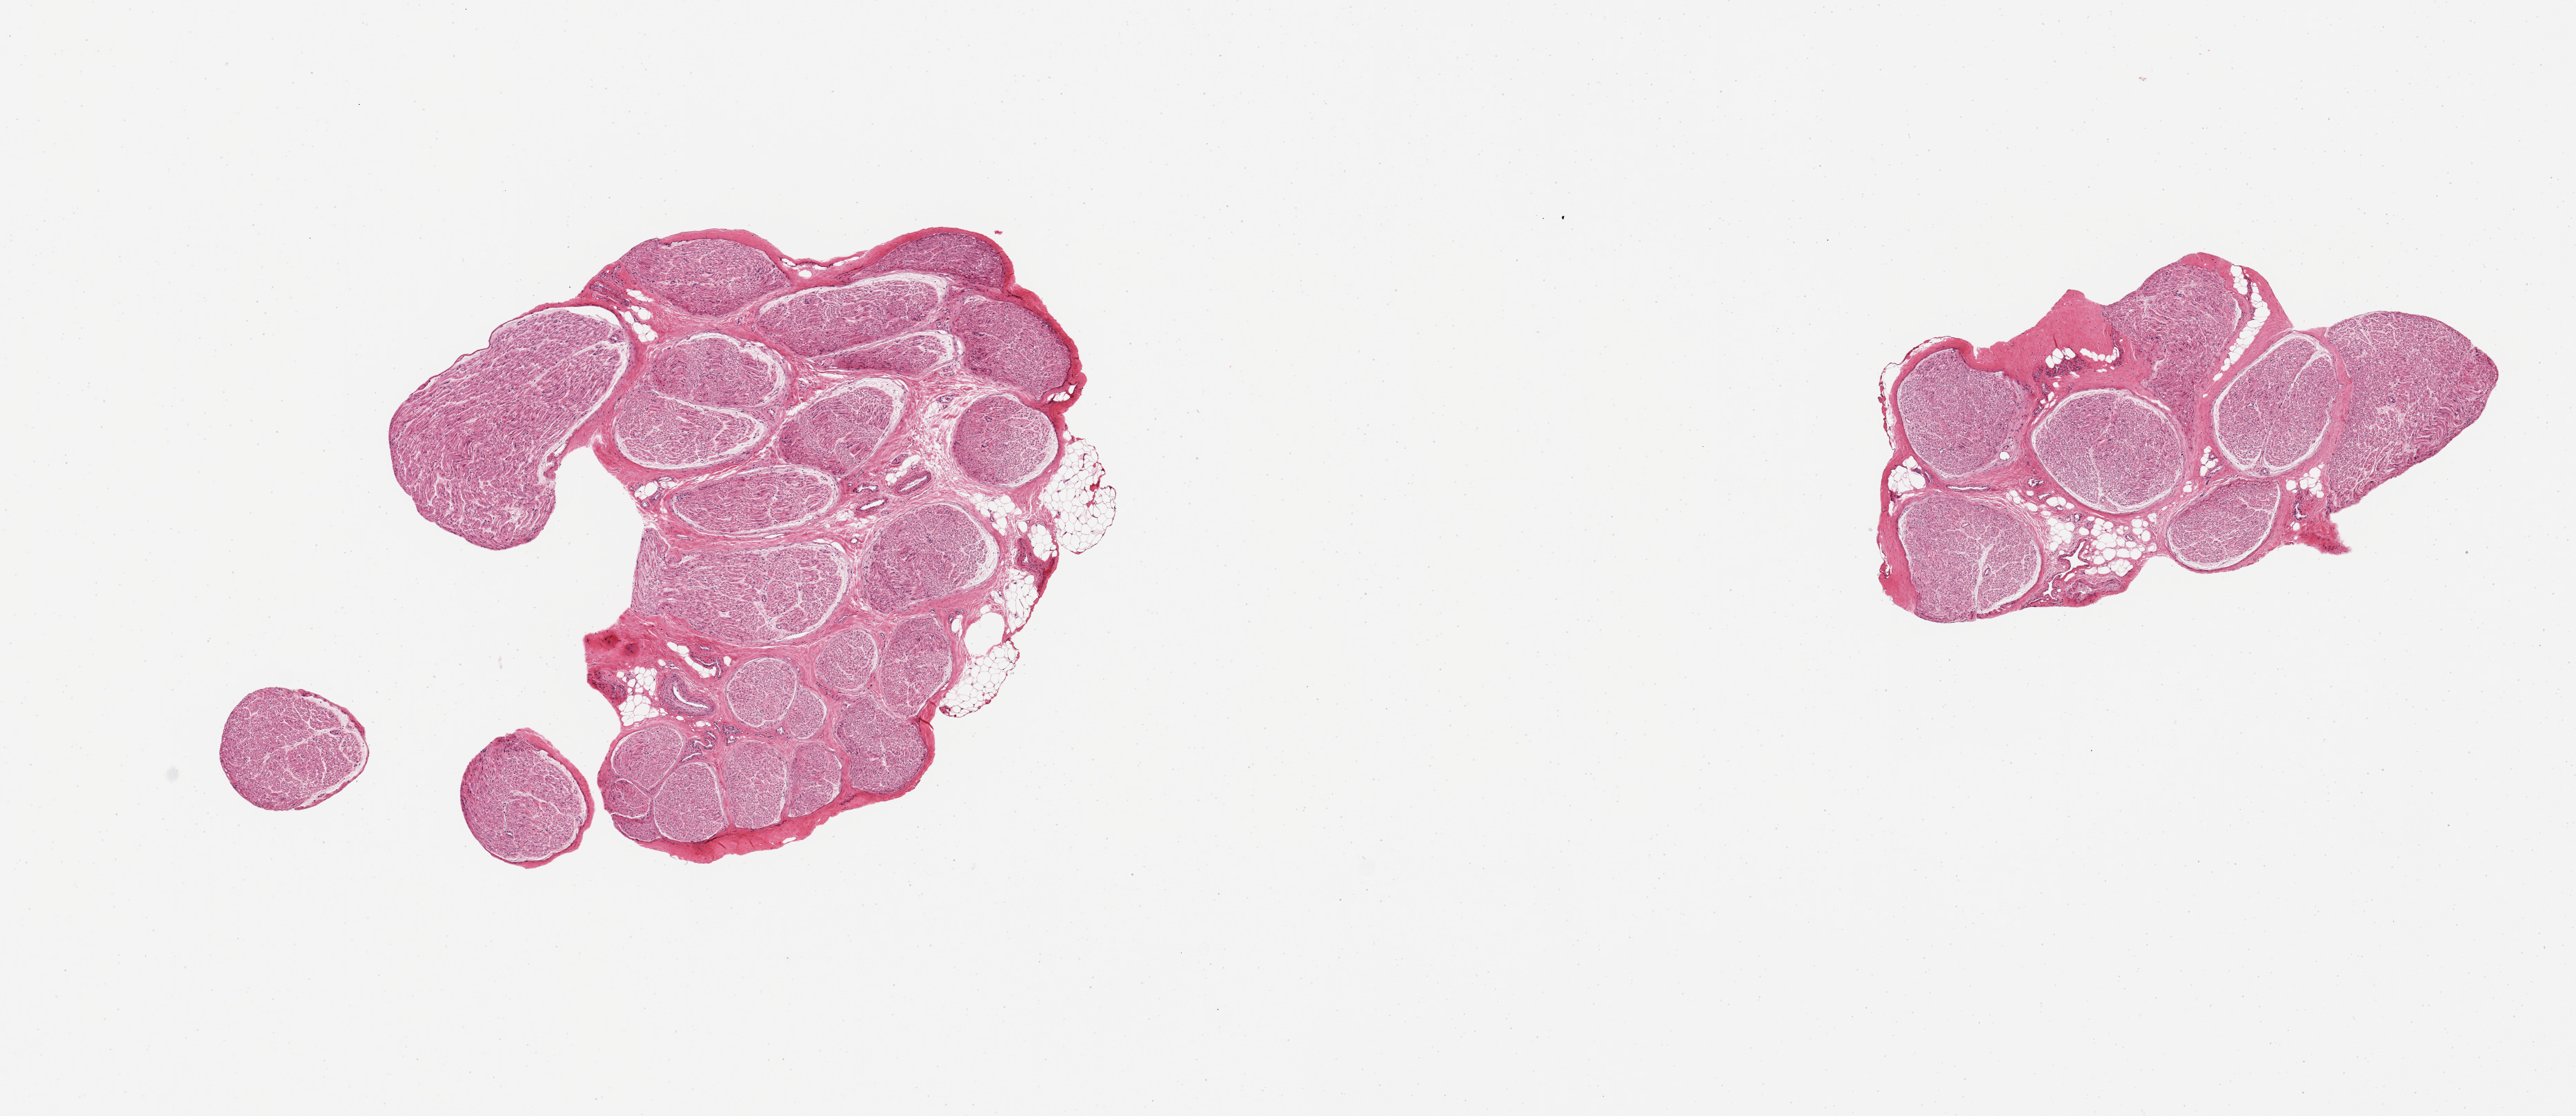
Digitized H&E-stained section, brightfield, shown as a low-resolution overview of the whole scanned area (about 14.8 x 6.4 mm), PAXgene-fixed paraffin-embedded (PFPE) section, section of tibial nerve (target tissue), donor tissue sample.
- review note (as recorded): 2 pieces; ~5% external fat